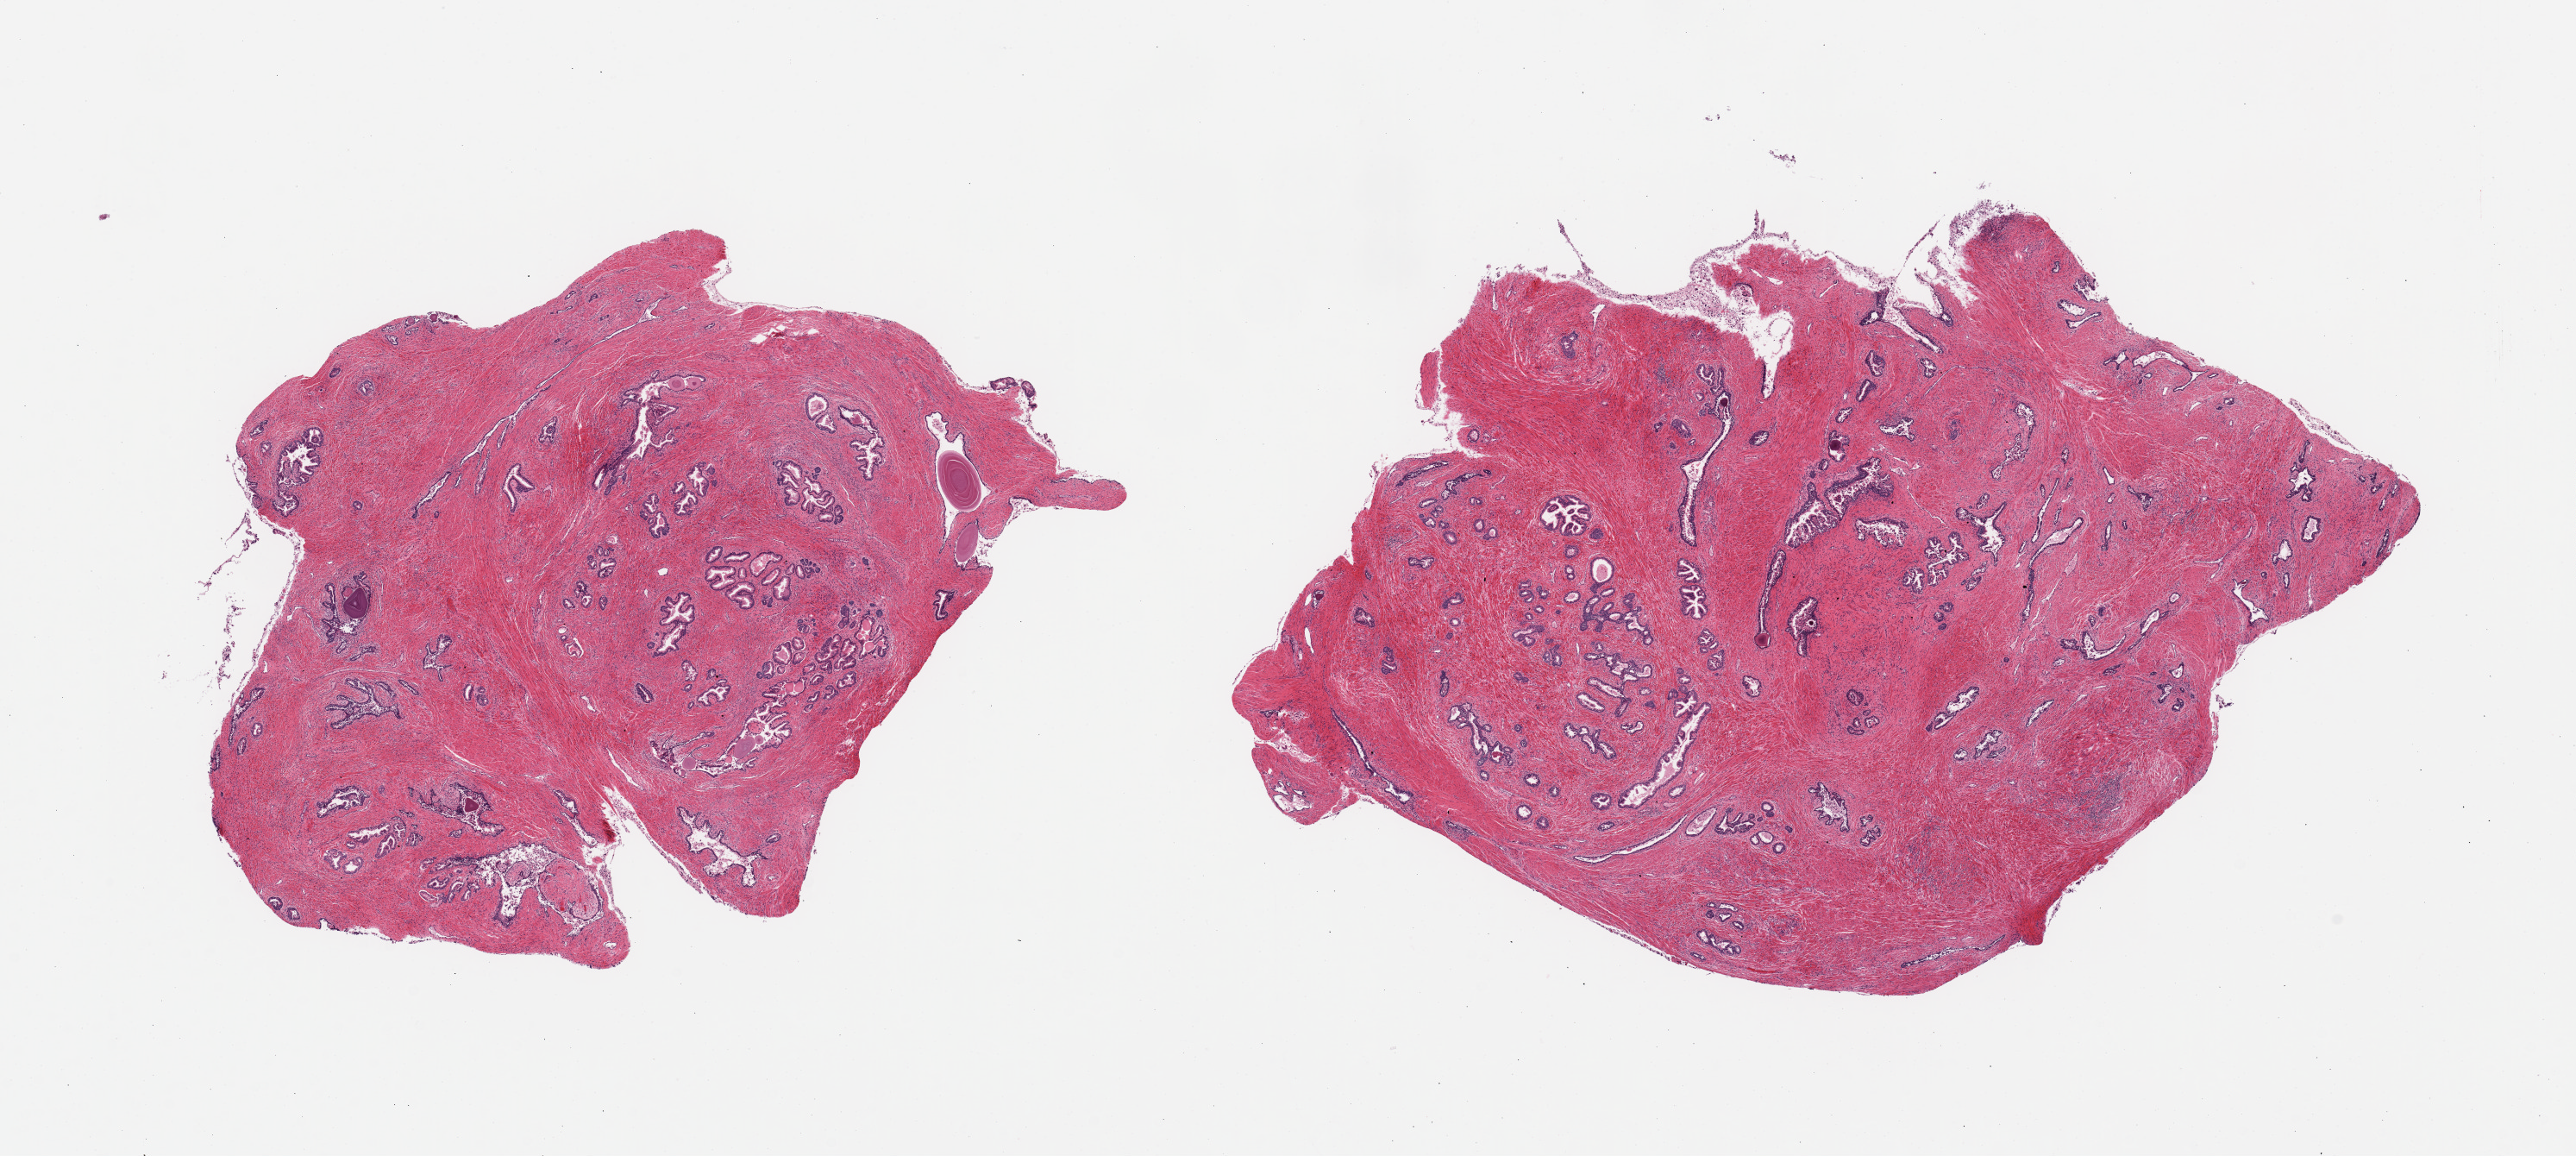
Haematoxylin and eosin whole-slide image, brightfield, whole scanned area (about 23.6 x 10.6 mm) shown as a low-resolution overview. PAXgene-fixed, paraffin-embedded tissue. Section of prostate (target tissue). Donor tissue sample. Male donor.
* reviewer comment on this tissue sample: 2 pieces; glands' autolysis varies from 1 to 2